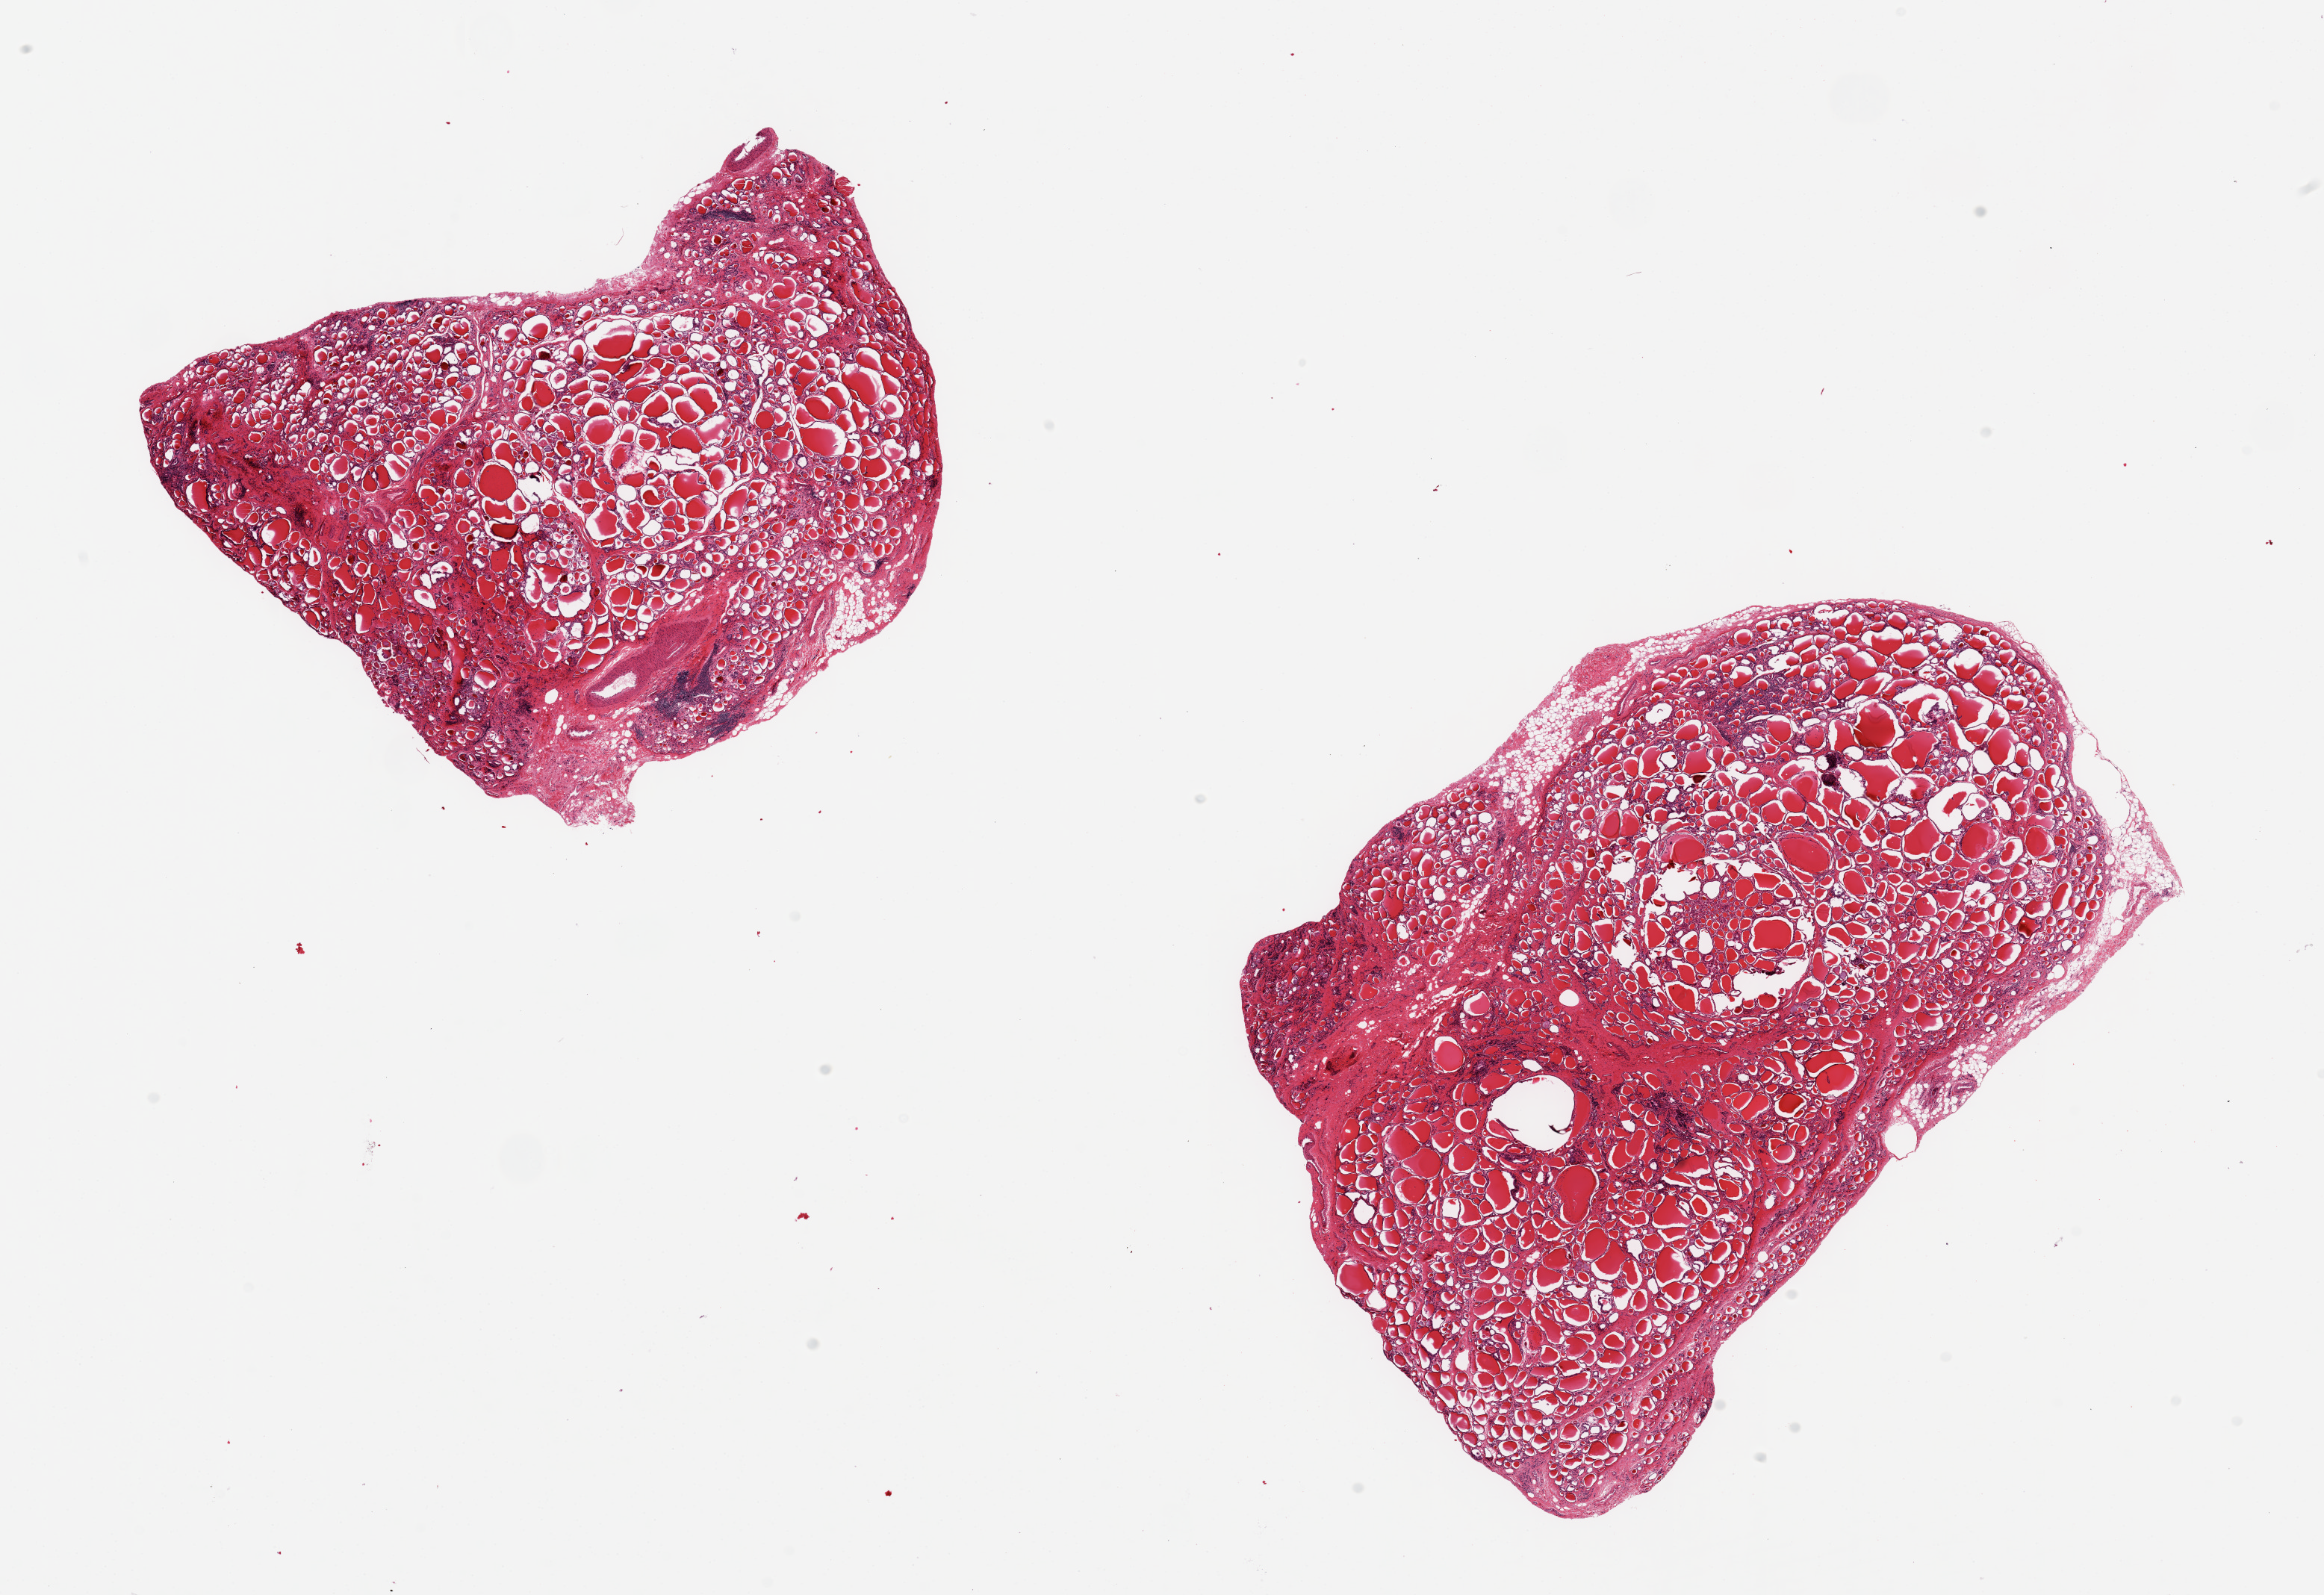
Hematoxylin and eosin (H&E) whole-slide image, shown as a low-resolution overview of the whole scanned area (about 24.6 x 16.9 mm, acquisition: 20x scan); PAXgene-fixed, paraffin-embedded tissue; section of thyroid (target tissue); donor tissue sample. Donor: female.
Reviewer comment on this tissue sample: 2 pieces ~8x7mm, focal areas of lymphocytic infiltrate c/w early Hashimoto's/lymphocytic thyroiditis. Less-well preserved than usual.